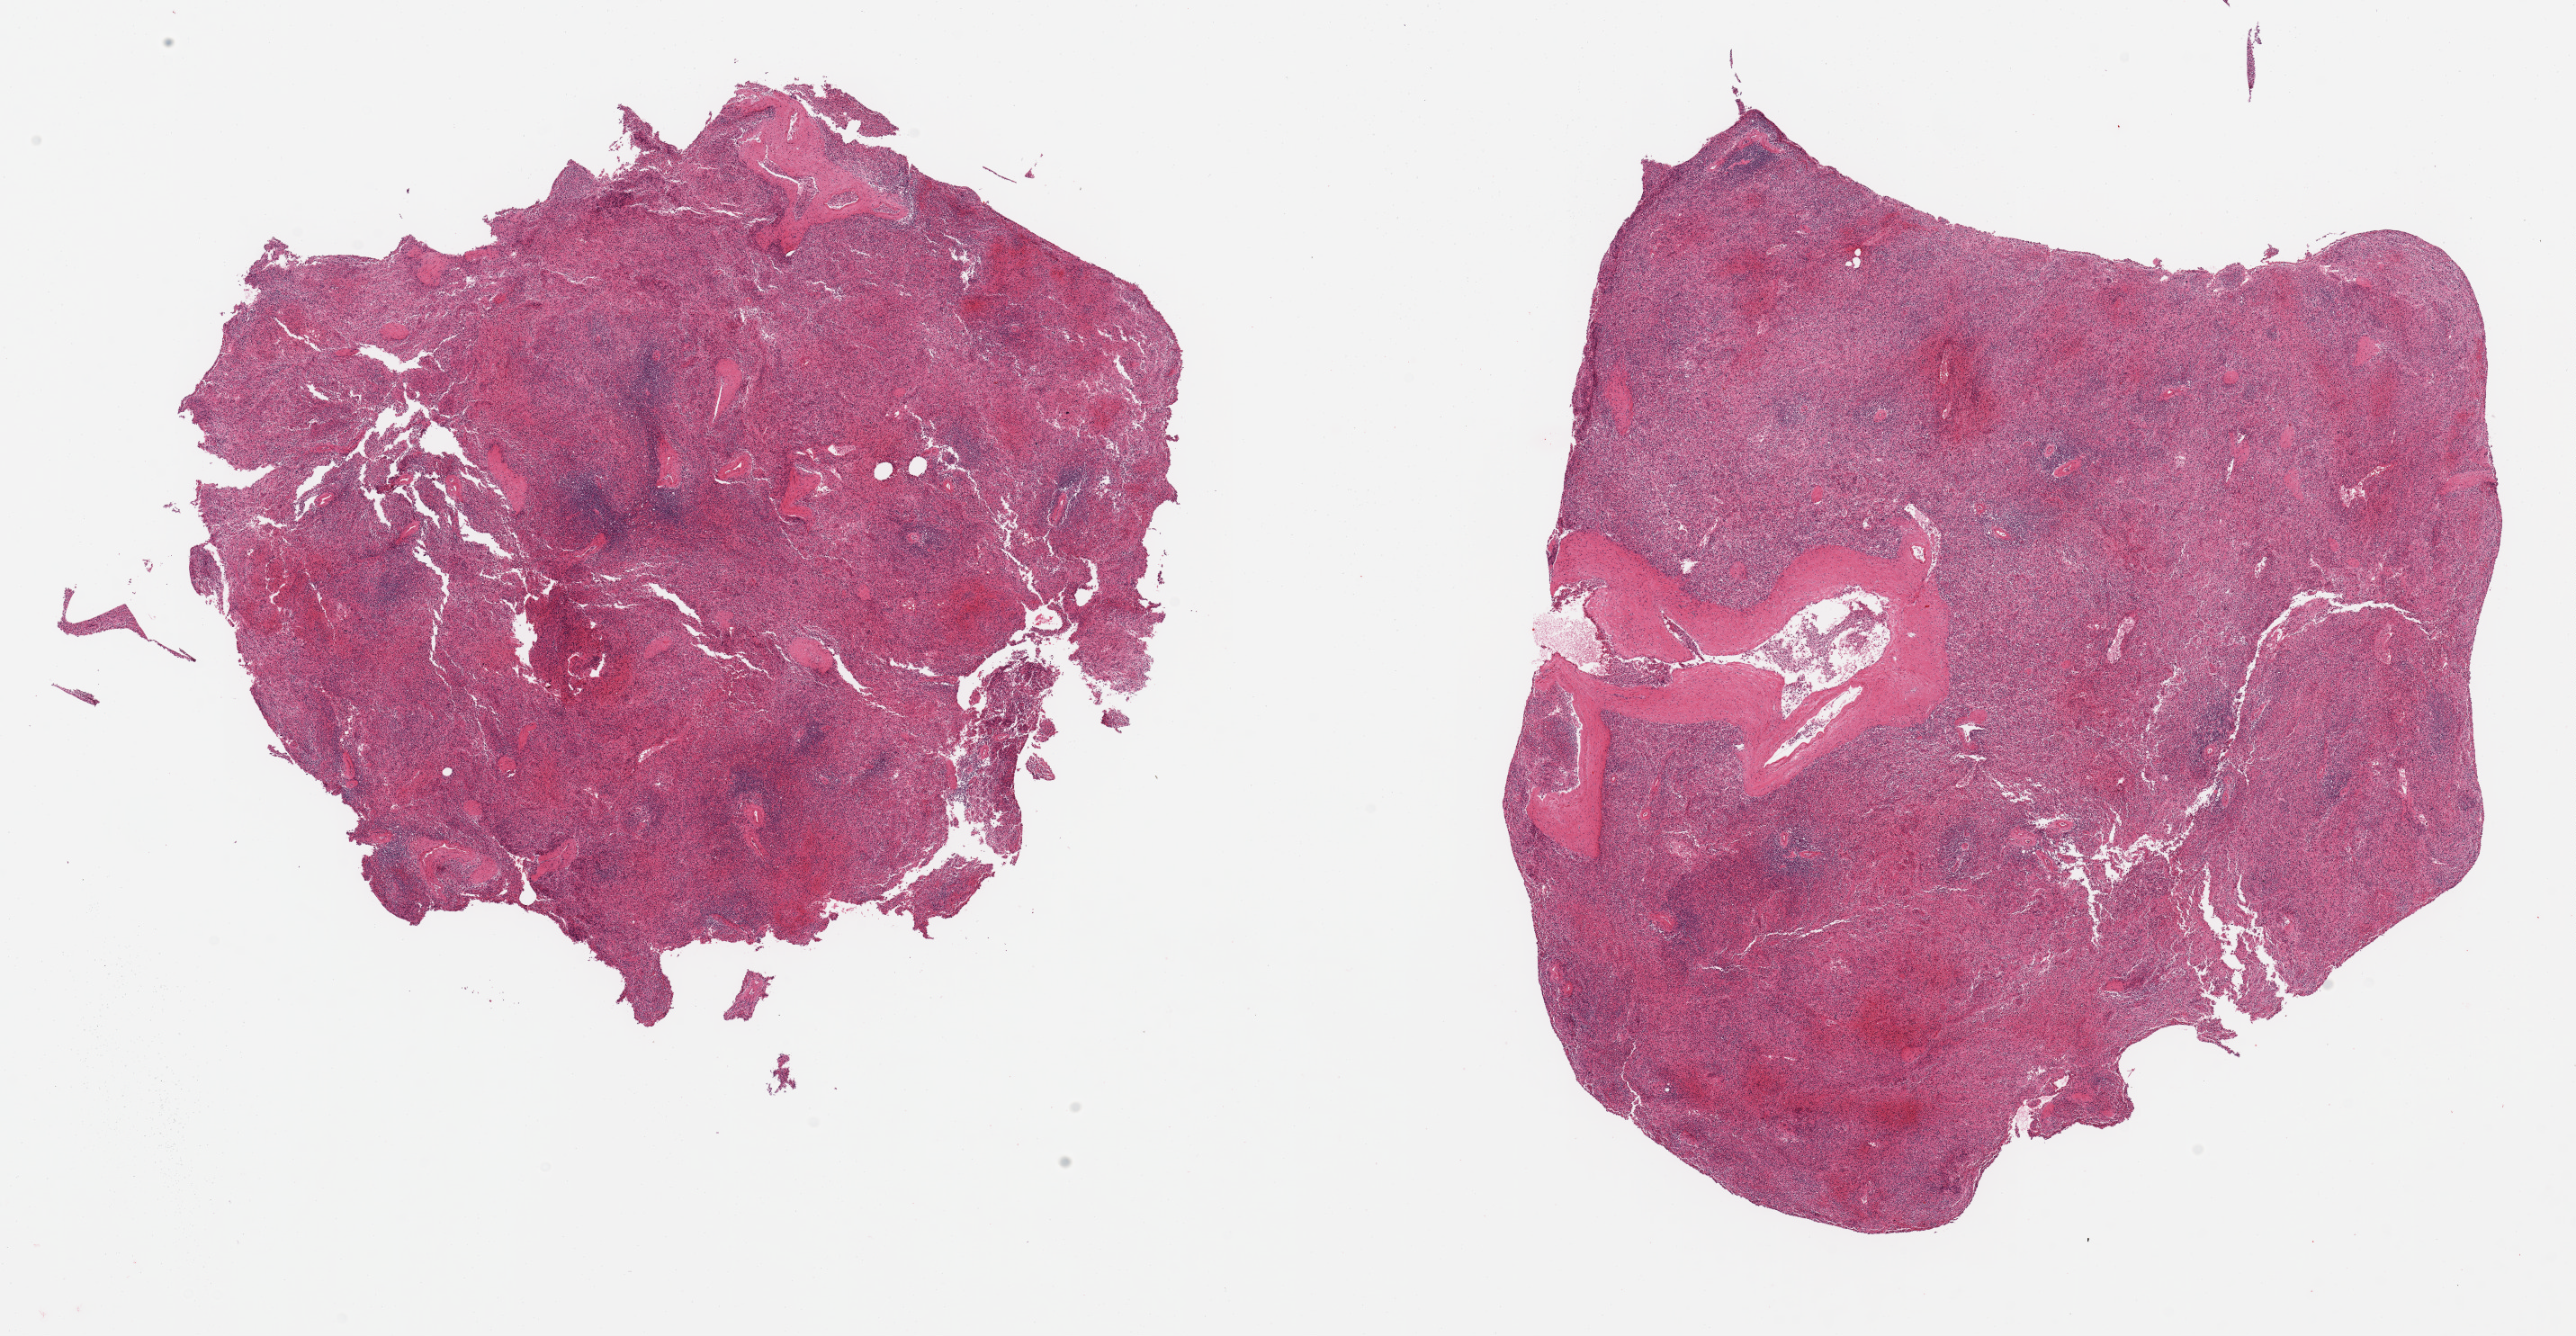
Hematoxylin and eosin (H&E) whole-slide image — a low-resolution overview of the entire scanned area, about 22.6 x 11.7 mm; PAXgene-fixed, paraffin-embedded tissue; section of spleen (target tissue); tissue donor sample. Male donor.
Reviewer comment on this tissue sample: 2 pieces; moderately congested; partially fragmented.